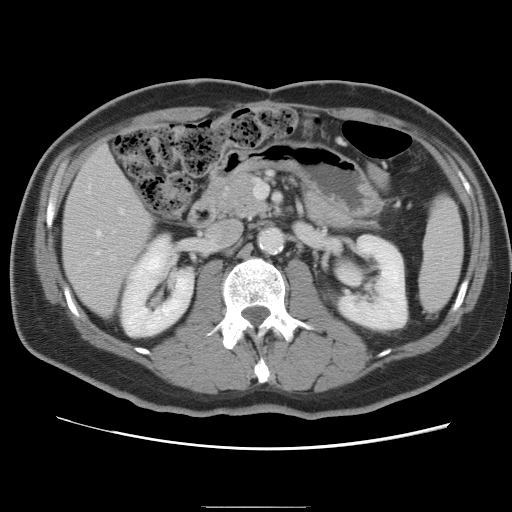
Contrast-enhanced abdominal CT, one axial slice. Slice 34 of 87 in the series (ordered by position). Intravenous contrast given. Soft-tissue window (W 400 / L 40 HU). 5 mm slice thickness. 512 × 512 image matrix. Male patient, age 63 years. Case-level facts recorded for this patient, not image findings: diagnosis: colorectal cancer liver metastases, imaged before liver resection; multiple liver metastases: no; largest metastasis: 9 cm.
Annotated regions visible in this slice (expert manual segmentation):
- hepatic veins: box from (x=96, y=231) to (x=101, y=253) px
- liver: (x=63, y=146)–(x=153, y=316)
- planned liver remnant (the part of the liver to remain after resection): (x=64, y=146)–(x=154, y=316)
- portal vein (with intrahepatic branches): (x=112, y=210)–(x=124, y=259)